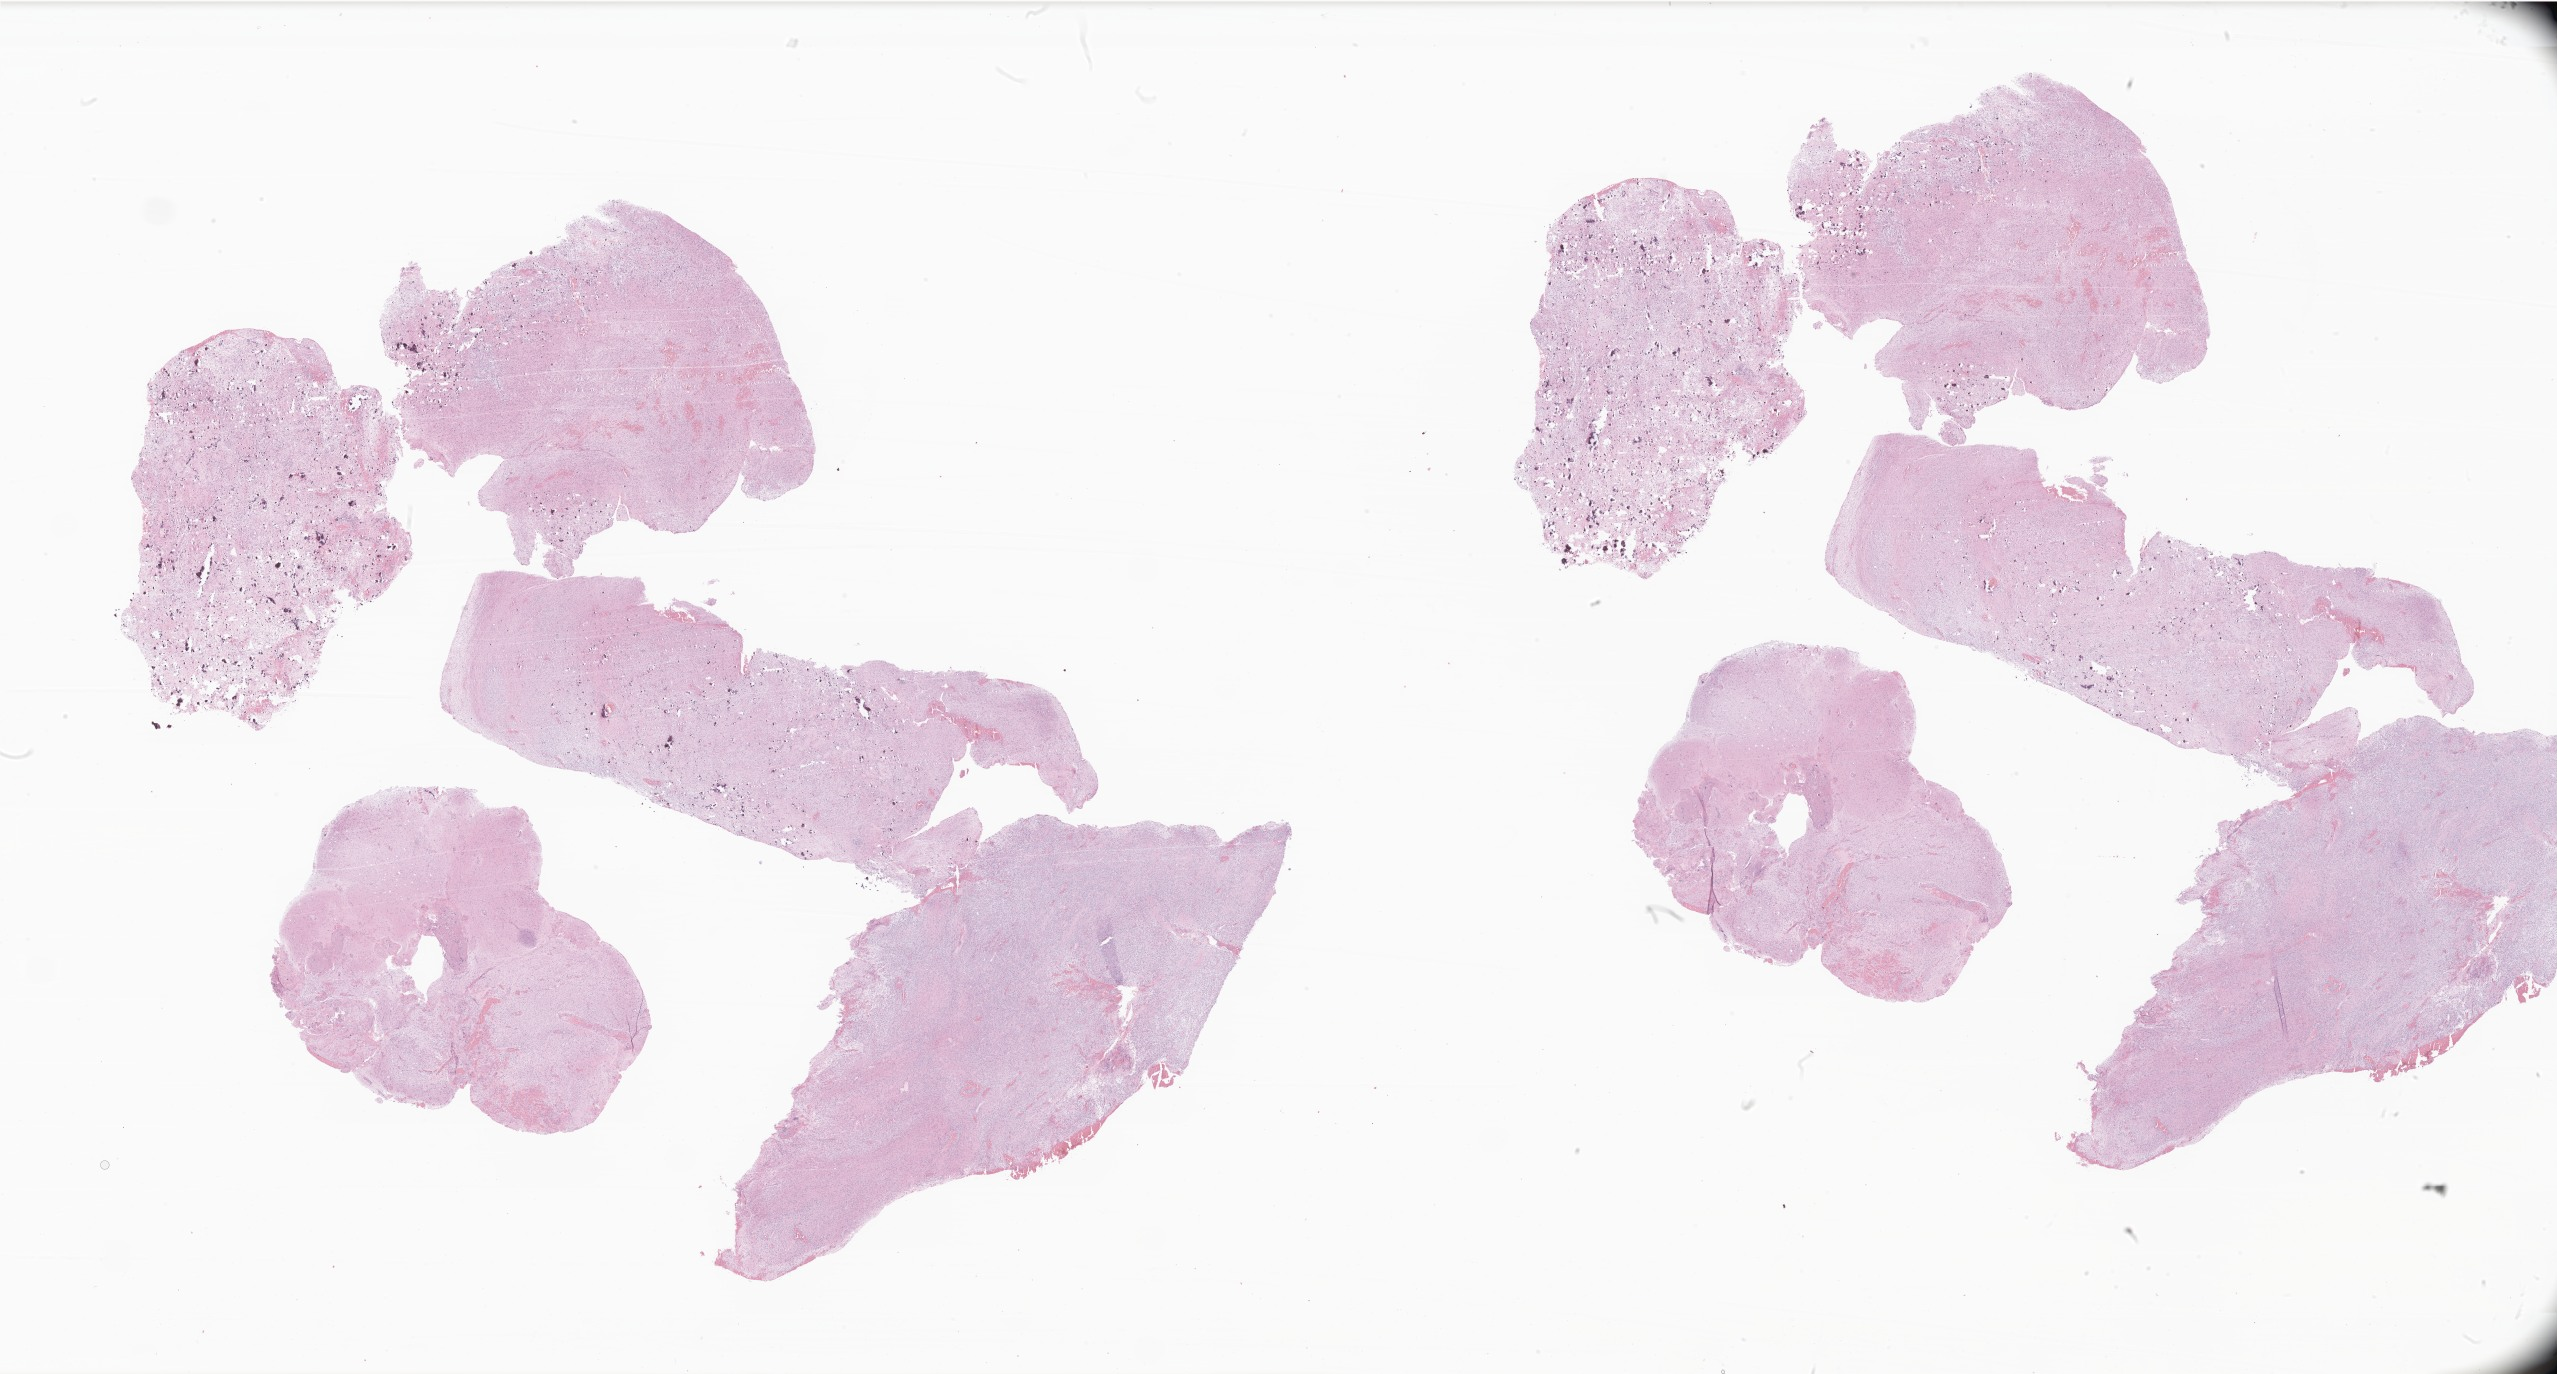
Haematoxylin and eosin whole-slide image of tumor tissue from the brain stem, low-resolution overview of the scanned area, about 43.1 x 23.2 mm, FFPE section. Female patient, age 55 months (4 years 7 months).
Recorded diagnosis: Pilocytic astrocytoma.